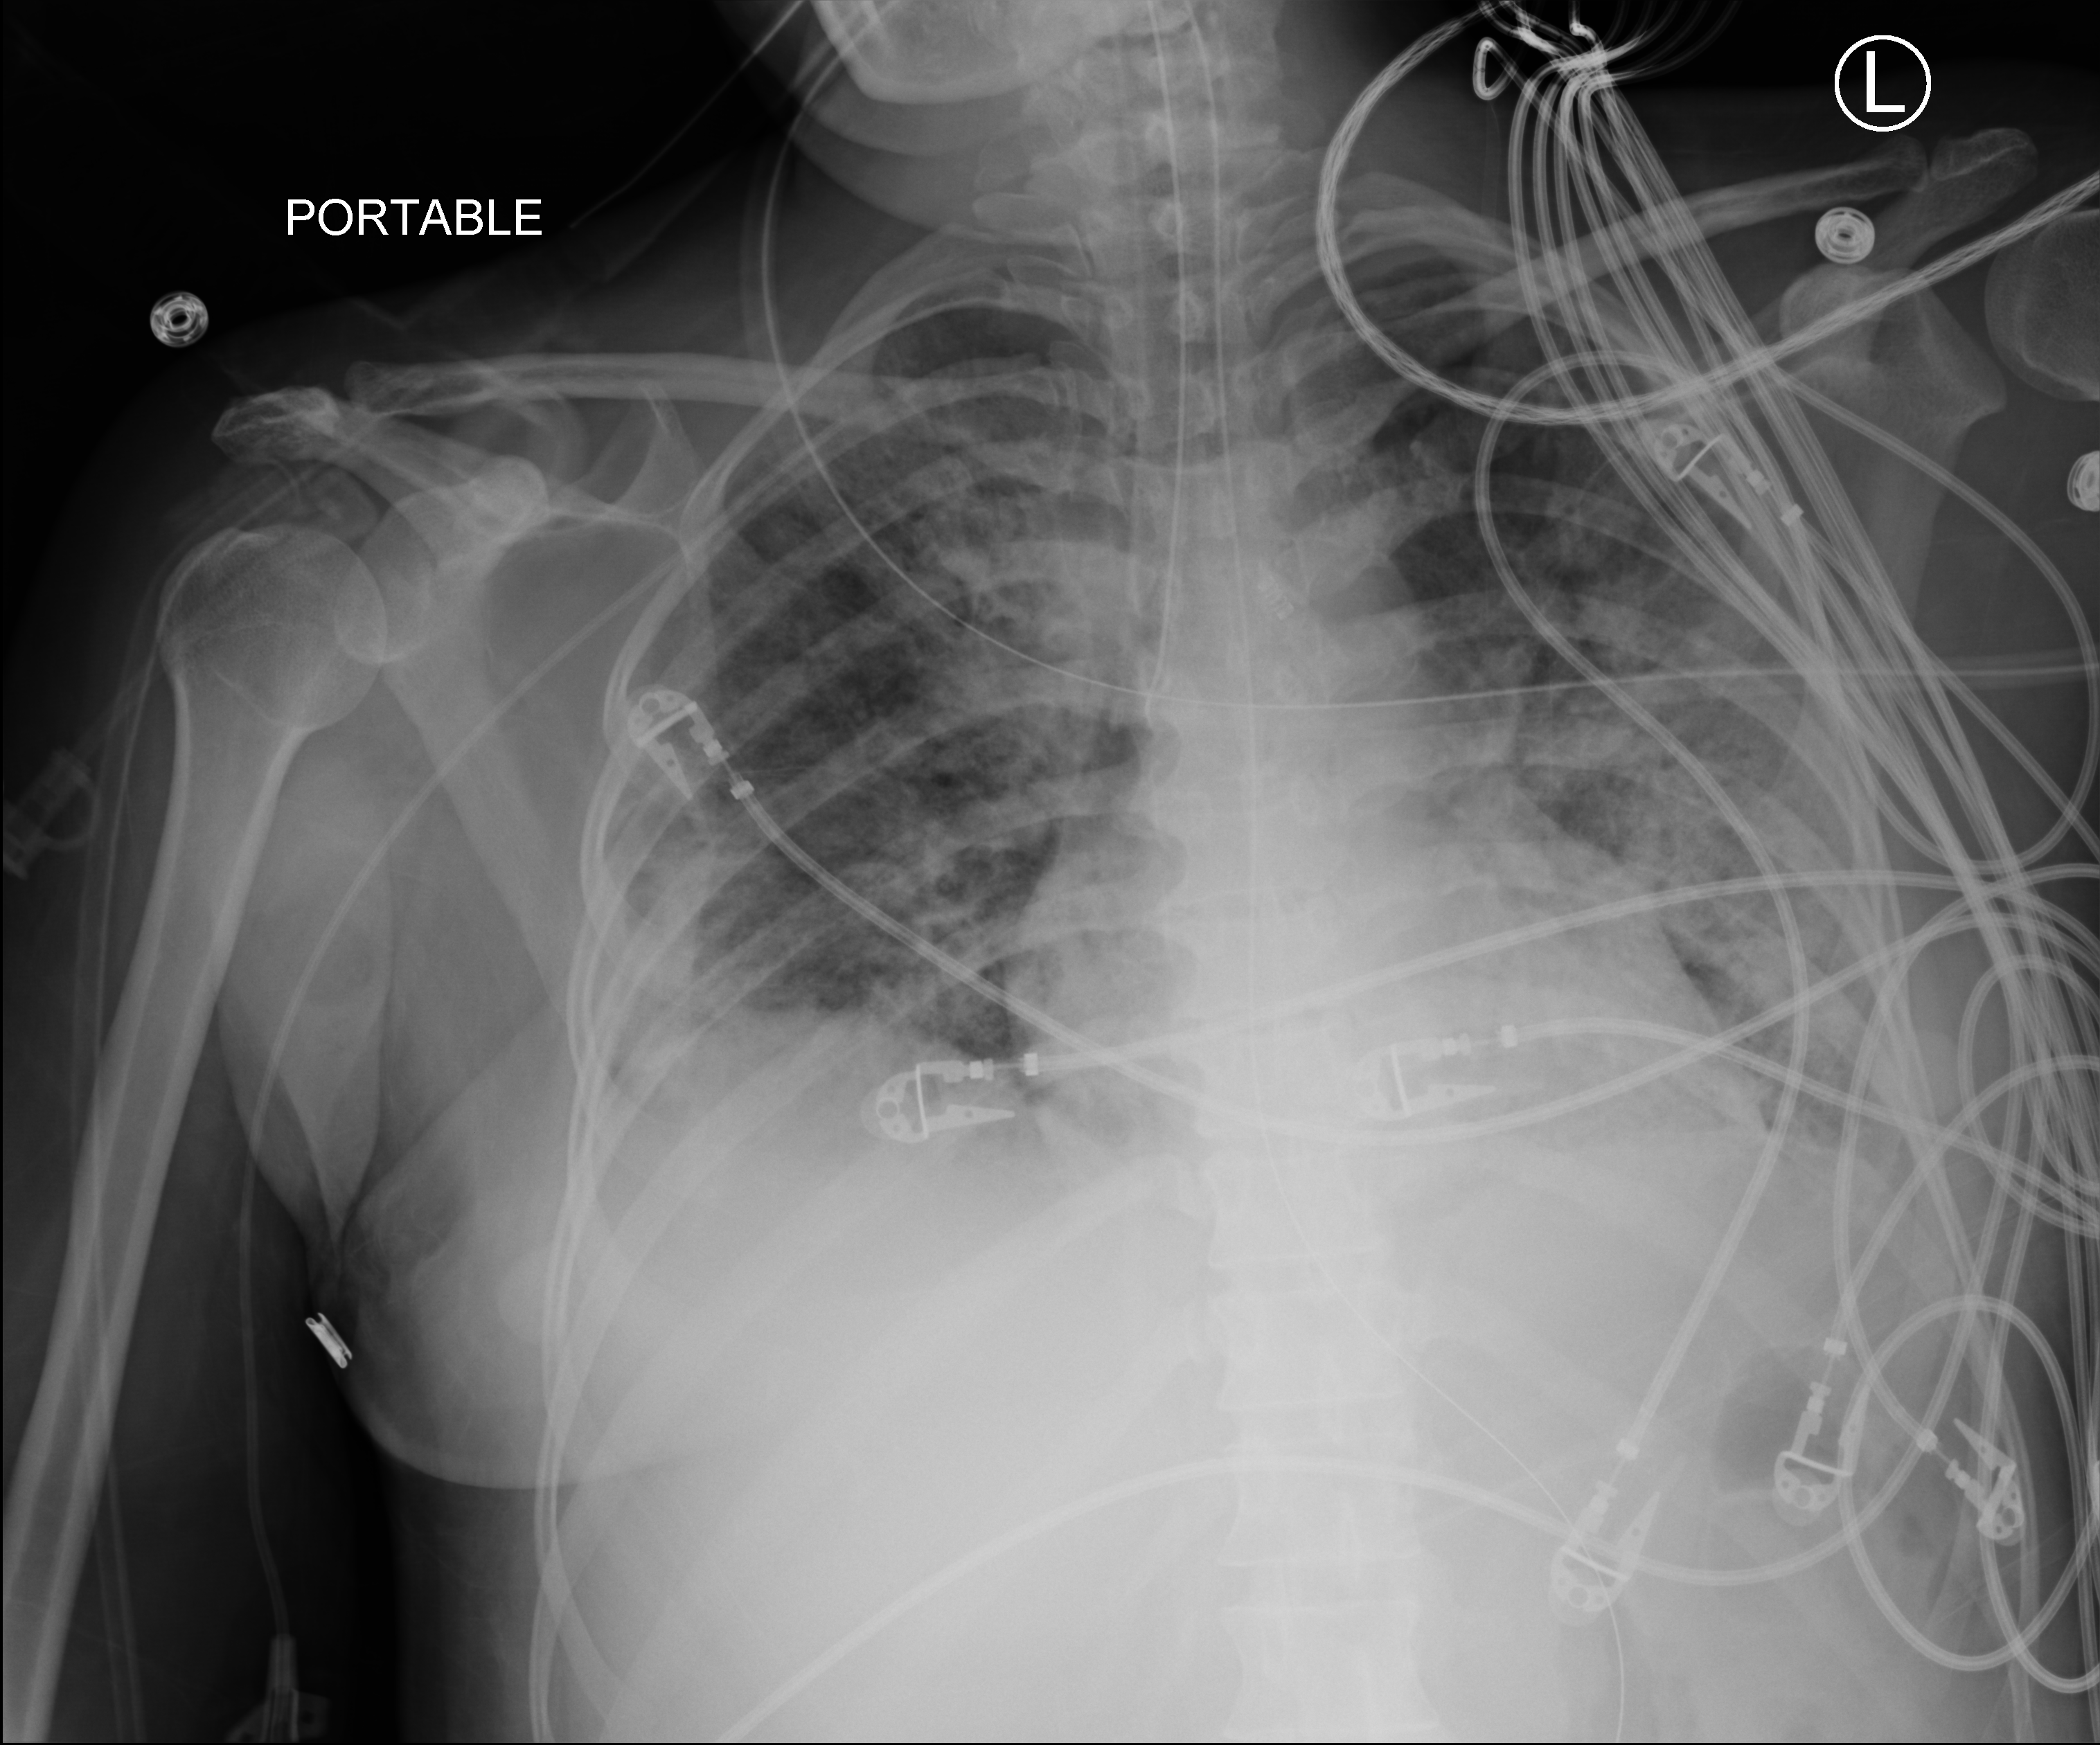
Portable chest radiograph, anteroposterior (AP) projection. Female patient hospitalised with COVID-19, age 18–59 years.
From the hospital-stay record, not from the radiograph (when in the stay this image was taken is not recorded): admitted to intensive care during this hospital stay: yes; smoking status (admission record): former; mechanically ventilated during this hospital stay: yes.